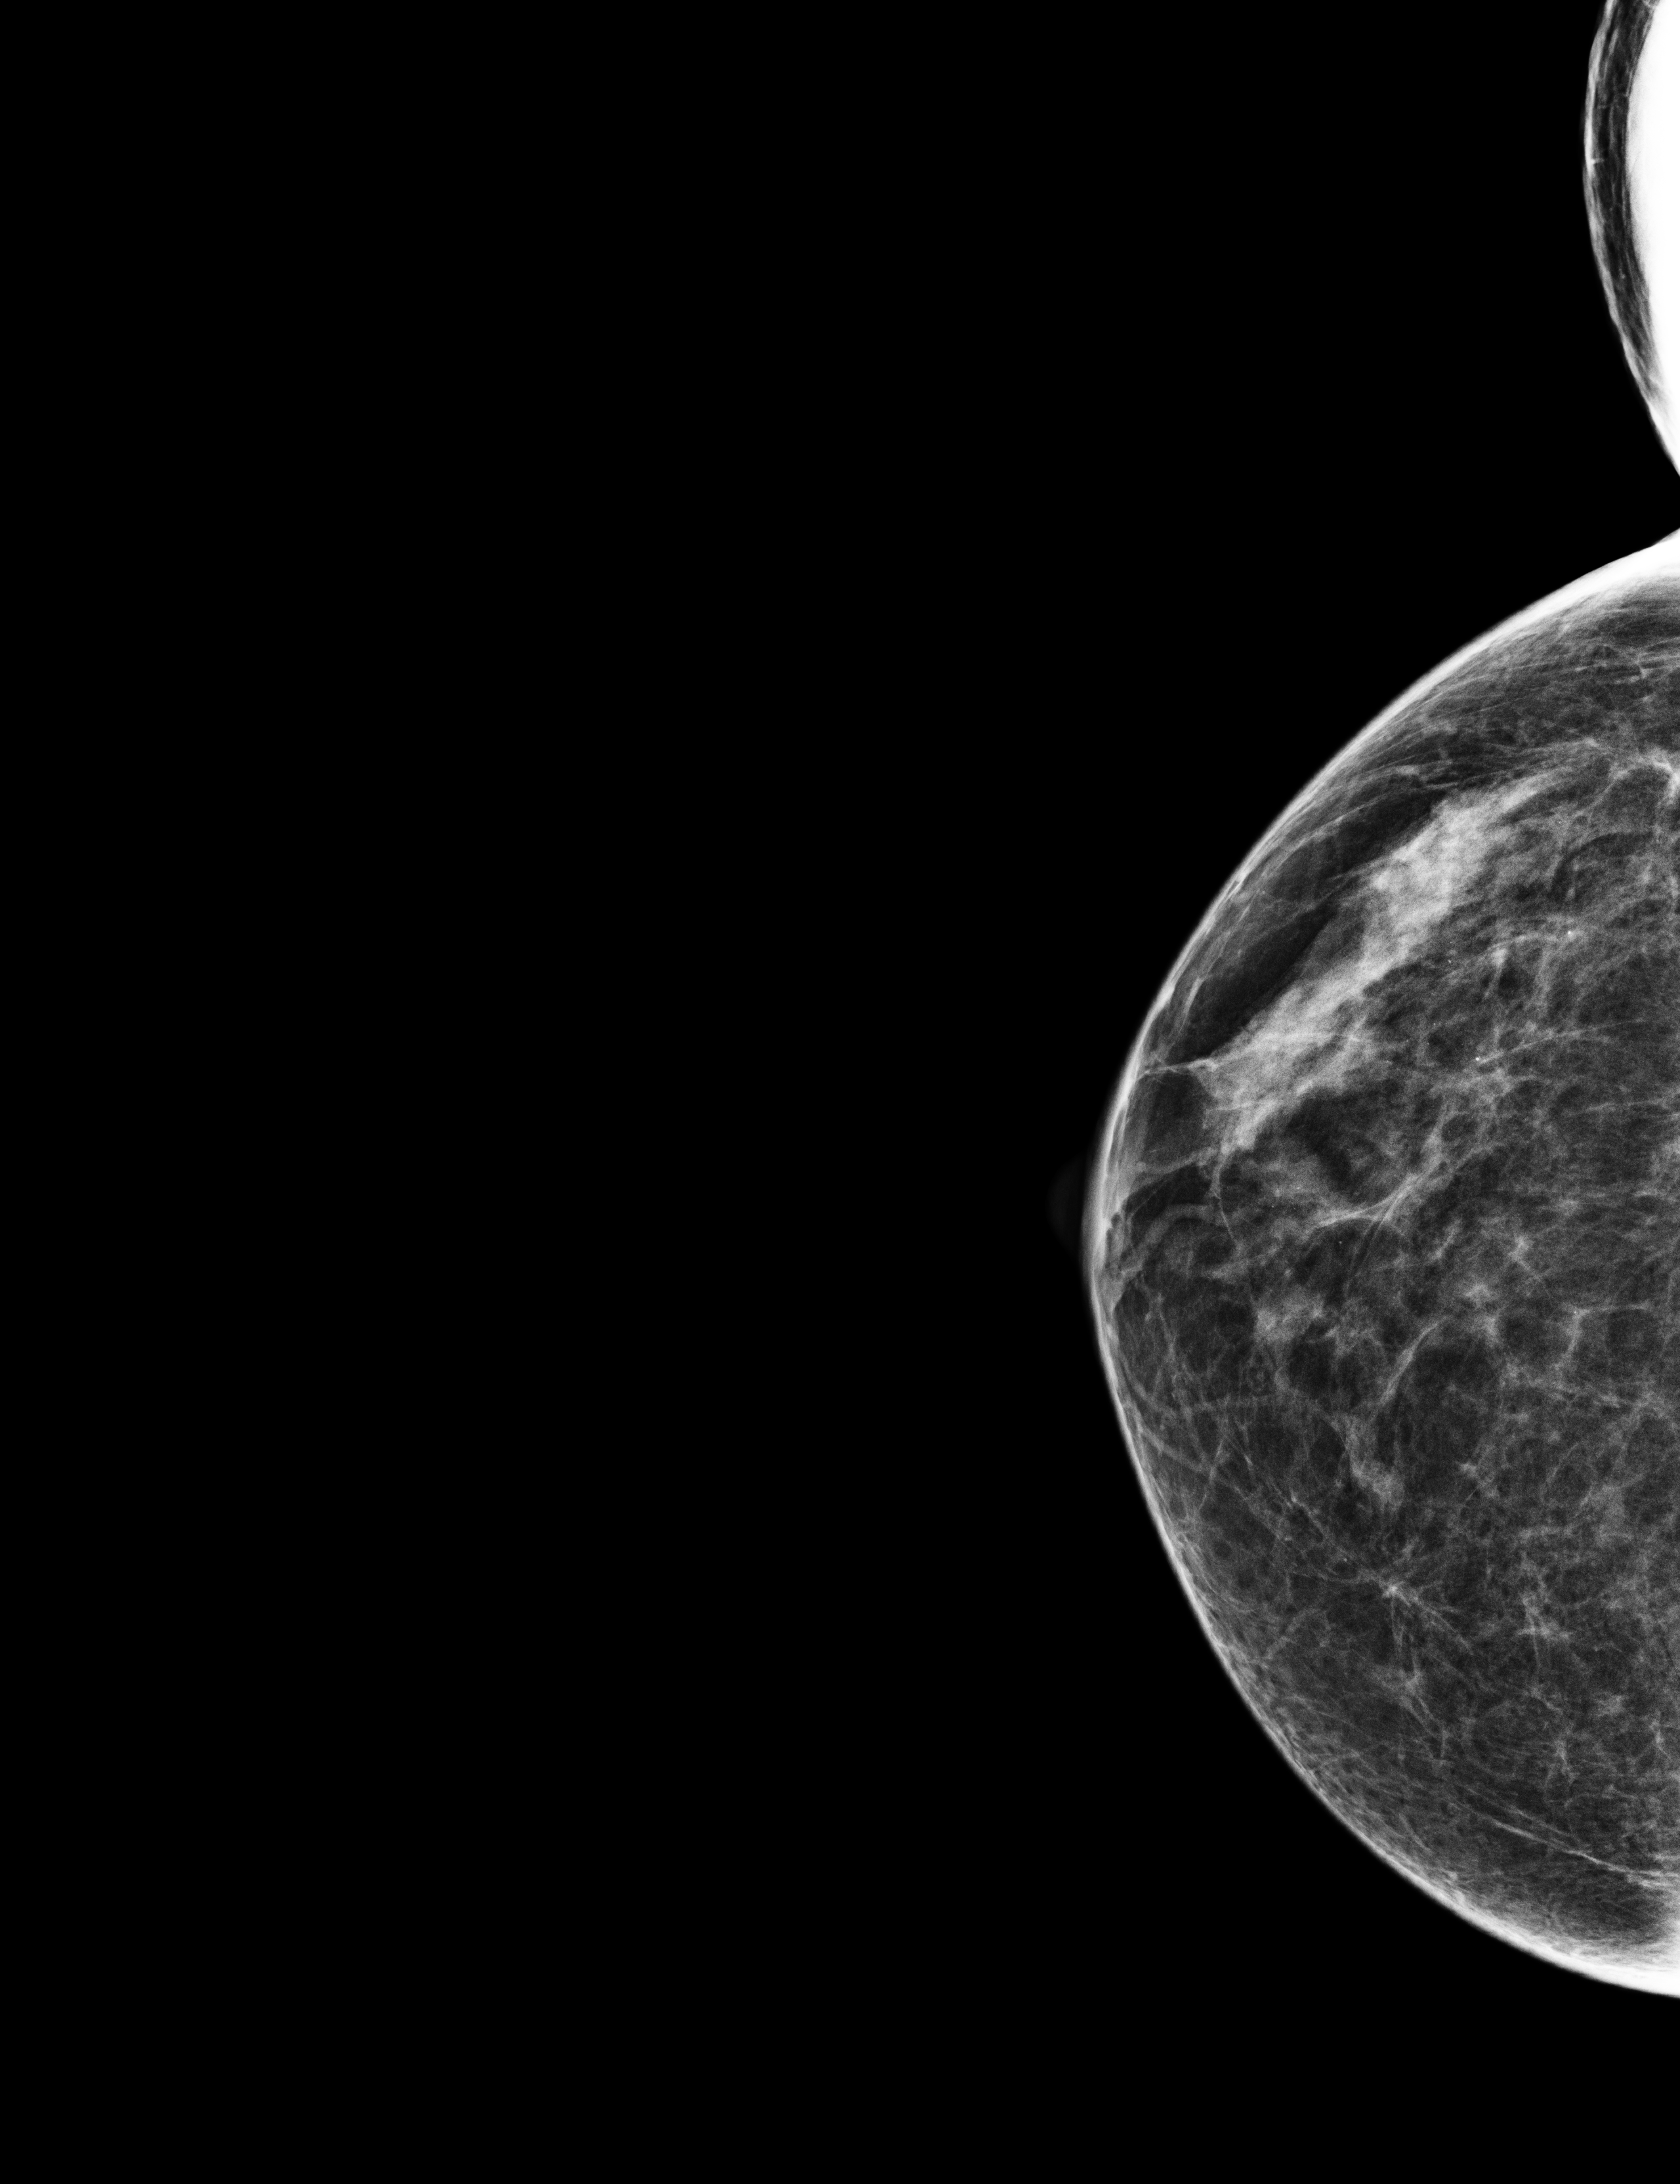
Annual screening mammography examination; compressed breast thickness 49 mm; system: Selenia Dimensions. Patient: female, 67 years.
Image type: full-field digital mammogram. Breast: right. Projection: cranio-caudal projection.